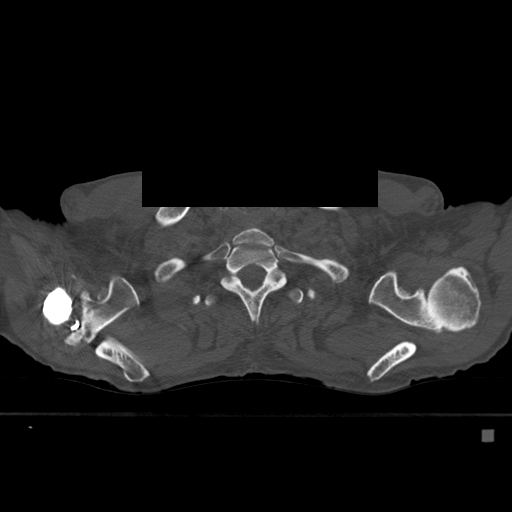
CT including the spine, one axial slice. Slice 445 of 527 in the series (ordered by position). Bone window (W 1800 / L 400 HU). 1.5 mm slice thickness. 512 × 512 image matrix, field of view 373 × 373 mm. Male patient, age 78 years. Case-level facts recorded for this patient, not image findings: primary cancer: prostate.
Annotated regions visible in this slice (semi-automatically segmented with operator editing):
- T1 vertebra: box from (x=234, y=227) to (x=274, y=245) px
- T2 vertebra: (x=221, y=234)–(x=287, y=322)
- T3 vertebra: (x=204, y=276)–(x=303, y=308)